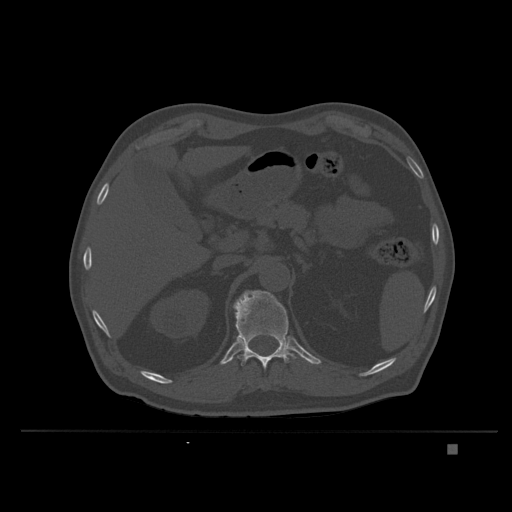
CT including the spine, one axial slice. Slice 159 of 435 in the series (ordered by position). Bone window (W 1800 / L 400 HU). 1.5 mm slice thickness. 512 × 512 image matrix, field of view 434 × 434 mm. Male patient, age 73 years. From the clinical record (not read from this slice): primary cancer: skin.
Outlined on this slice (semi-automatic segmentation, software-assisted and operator-edited):
- T12 vertebra: bounding box (x1, y1, x2, y2) in pixels: (233, 290, 297, 370)